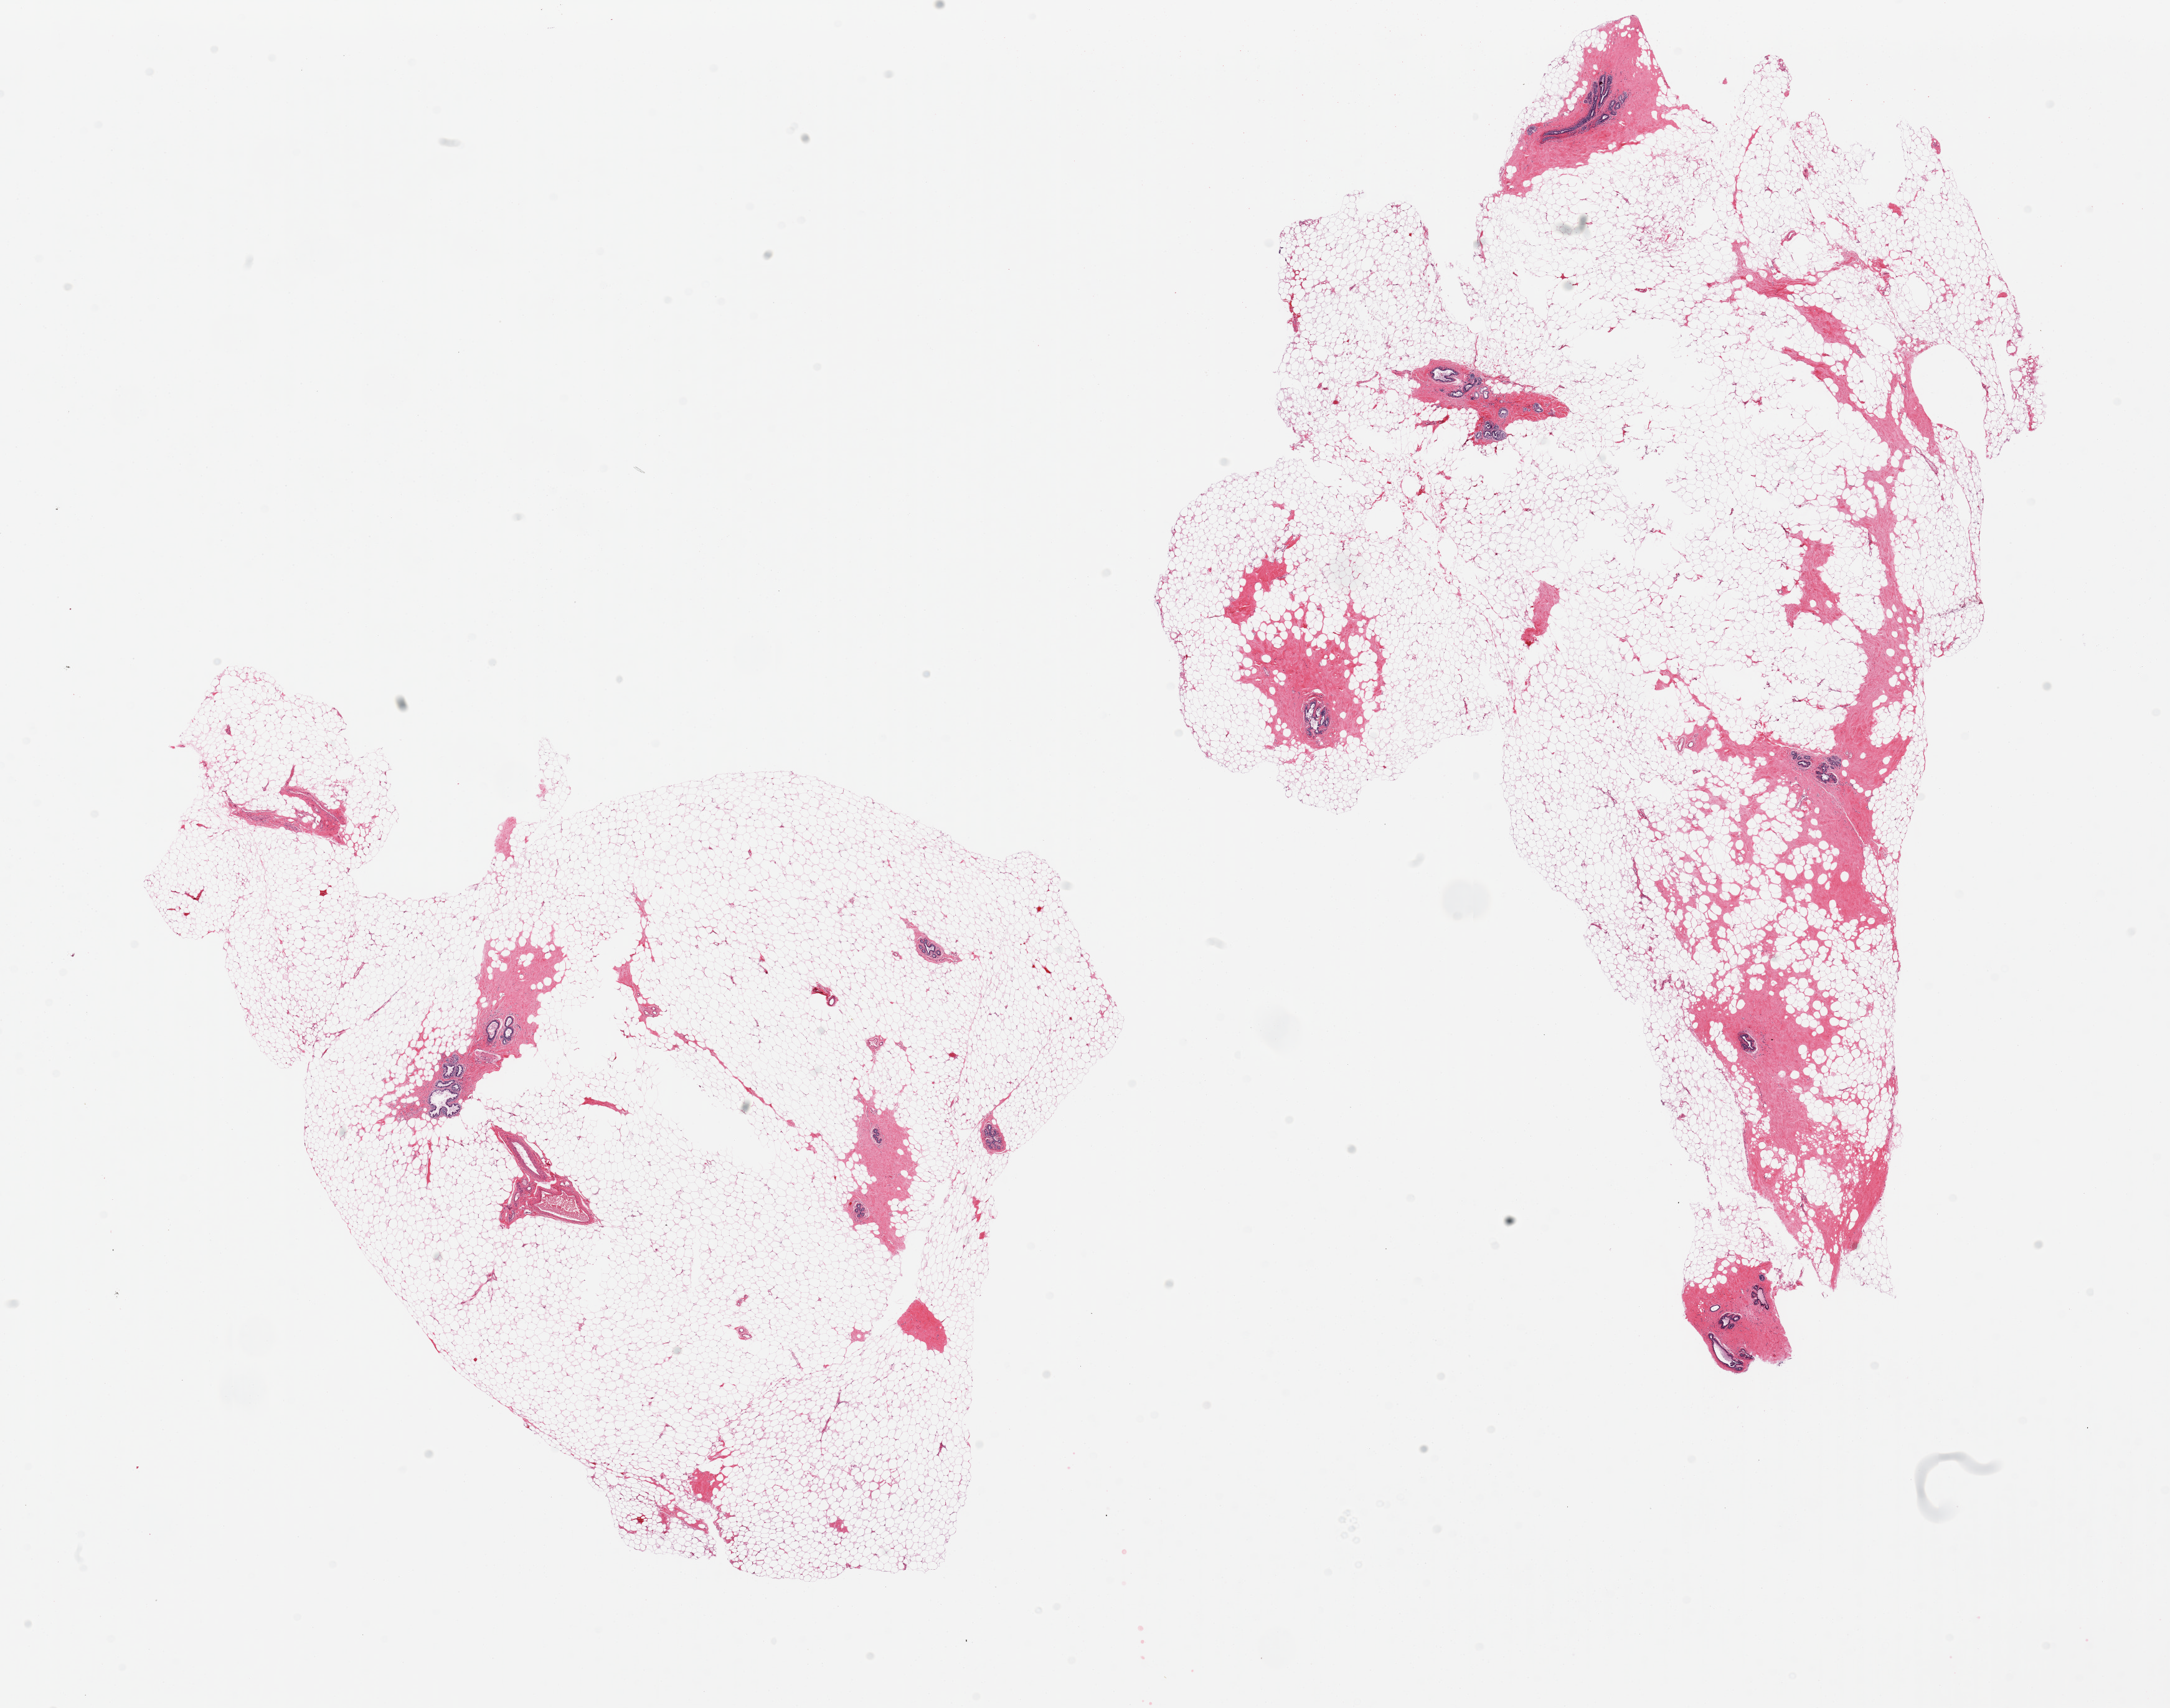
Whole-slide image, H&E stain, a low-resolution overview of the entire scanned area, about 27.6 x 21.7 mm (slide scanned at 20x). PAXgene-fixed, paraffin-embedded tissue. Section of breast (target tissue). Tissue donor sample. Donor: female.
• review note (as recorded): 2 pieces; largely fatty, atrophic ductal tissue